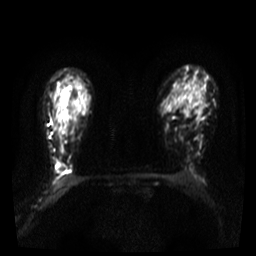
Breast MRI, one axial slice; position 26 of 36 along the scan axis; diffusion-weighted series; image 2 of 4 stored at this slice position (different b-values; order by instance number); 3 T; 5 mm slice thickness; 256 × 256 image matrix. Female patient.
Outlined on this slice (expert manual segmentation):
- tumour on diffusion-weighted imaging: bounding box <57,163,65,172> (left, top, right, bottom; pixels)